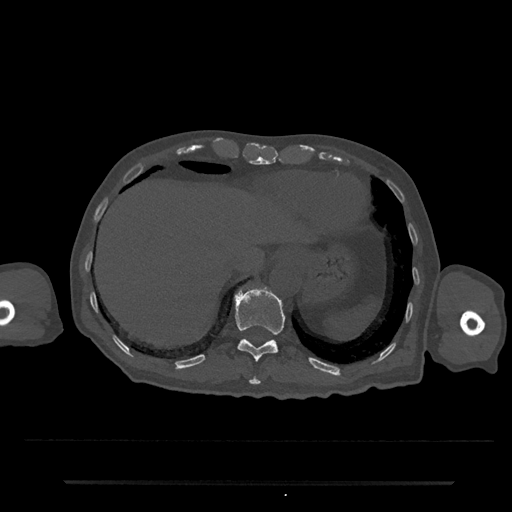
CT including the spine, one axial slice; position 253 of 797 along the scan axis; reconstruction kernel Br40s/3; bone window (W 1800 / L 400 HU); 0.5 mm slice thickness; 512 × 512 image matrix, field of view 427 × 427 mm. Male patient, age 74 years. Case-level facts recorded for this patient, not image findings: primary cancer: prostate.
Annotated regions visible in this slice (semi-automatically segmented with operator editing):
- T10 vertebra: bounding box [x1, y1, x2, y2] px = [249, 376, 261, 385]
- T11 vertebra: [234, 286, 285, 362]